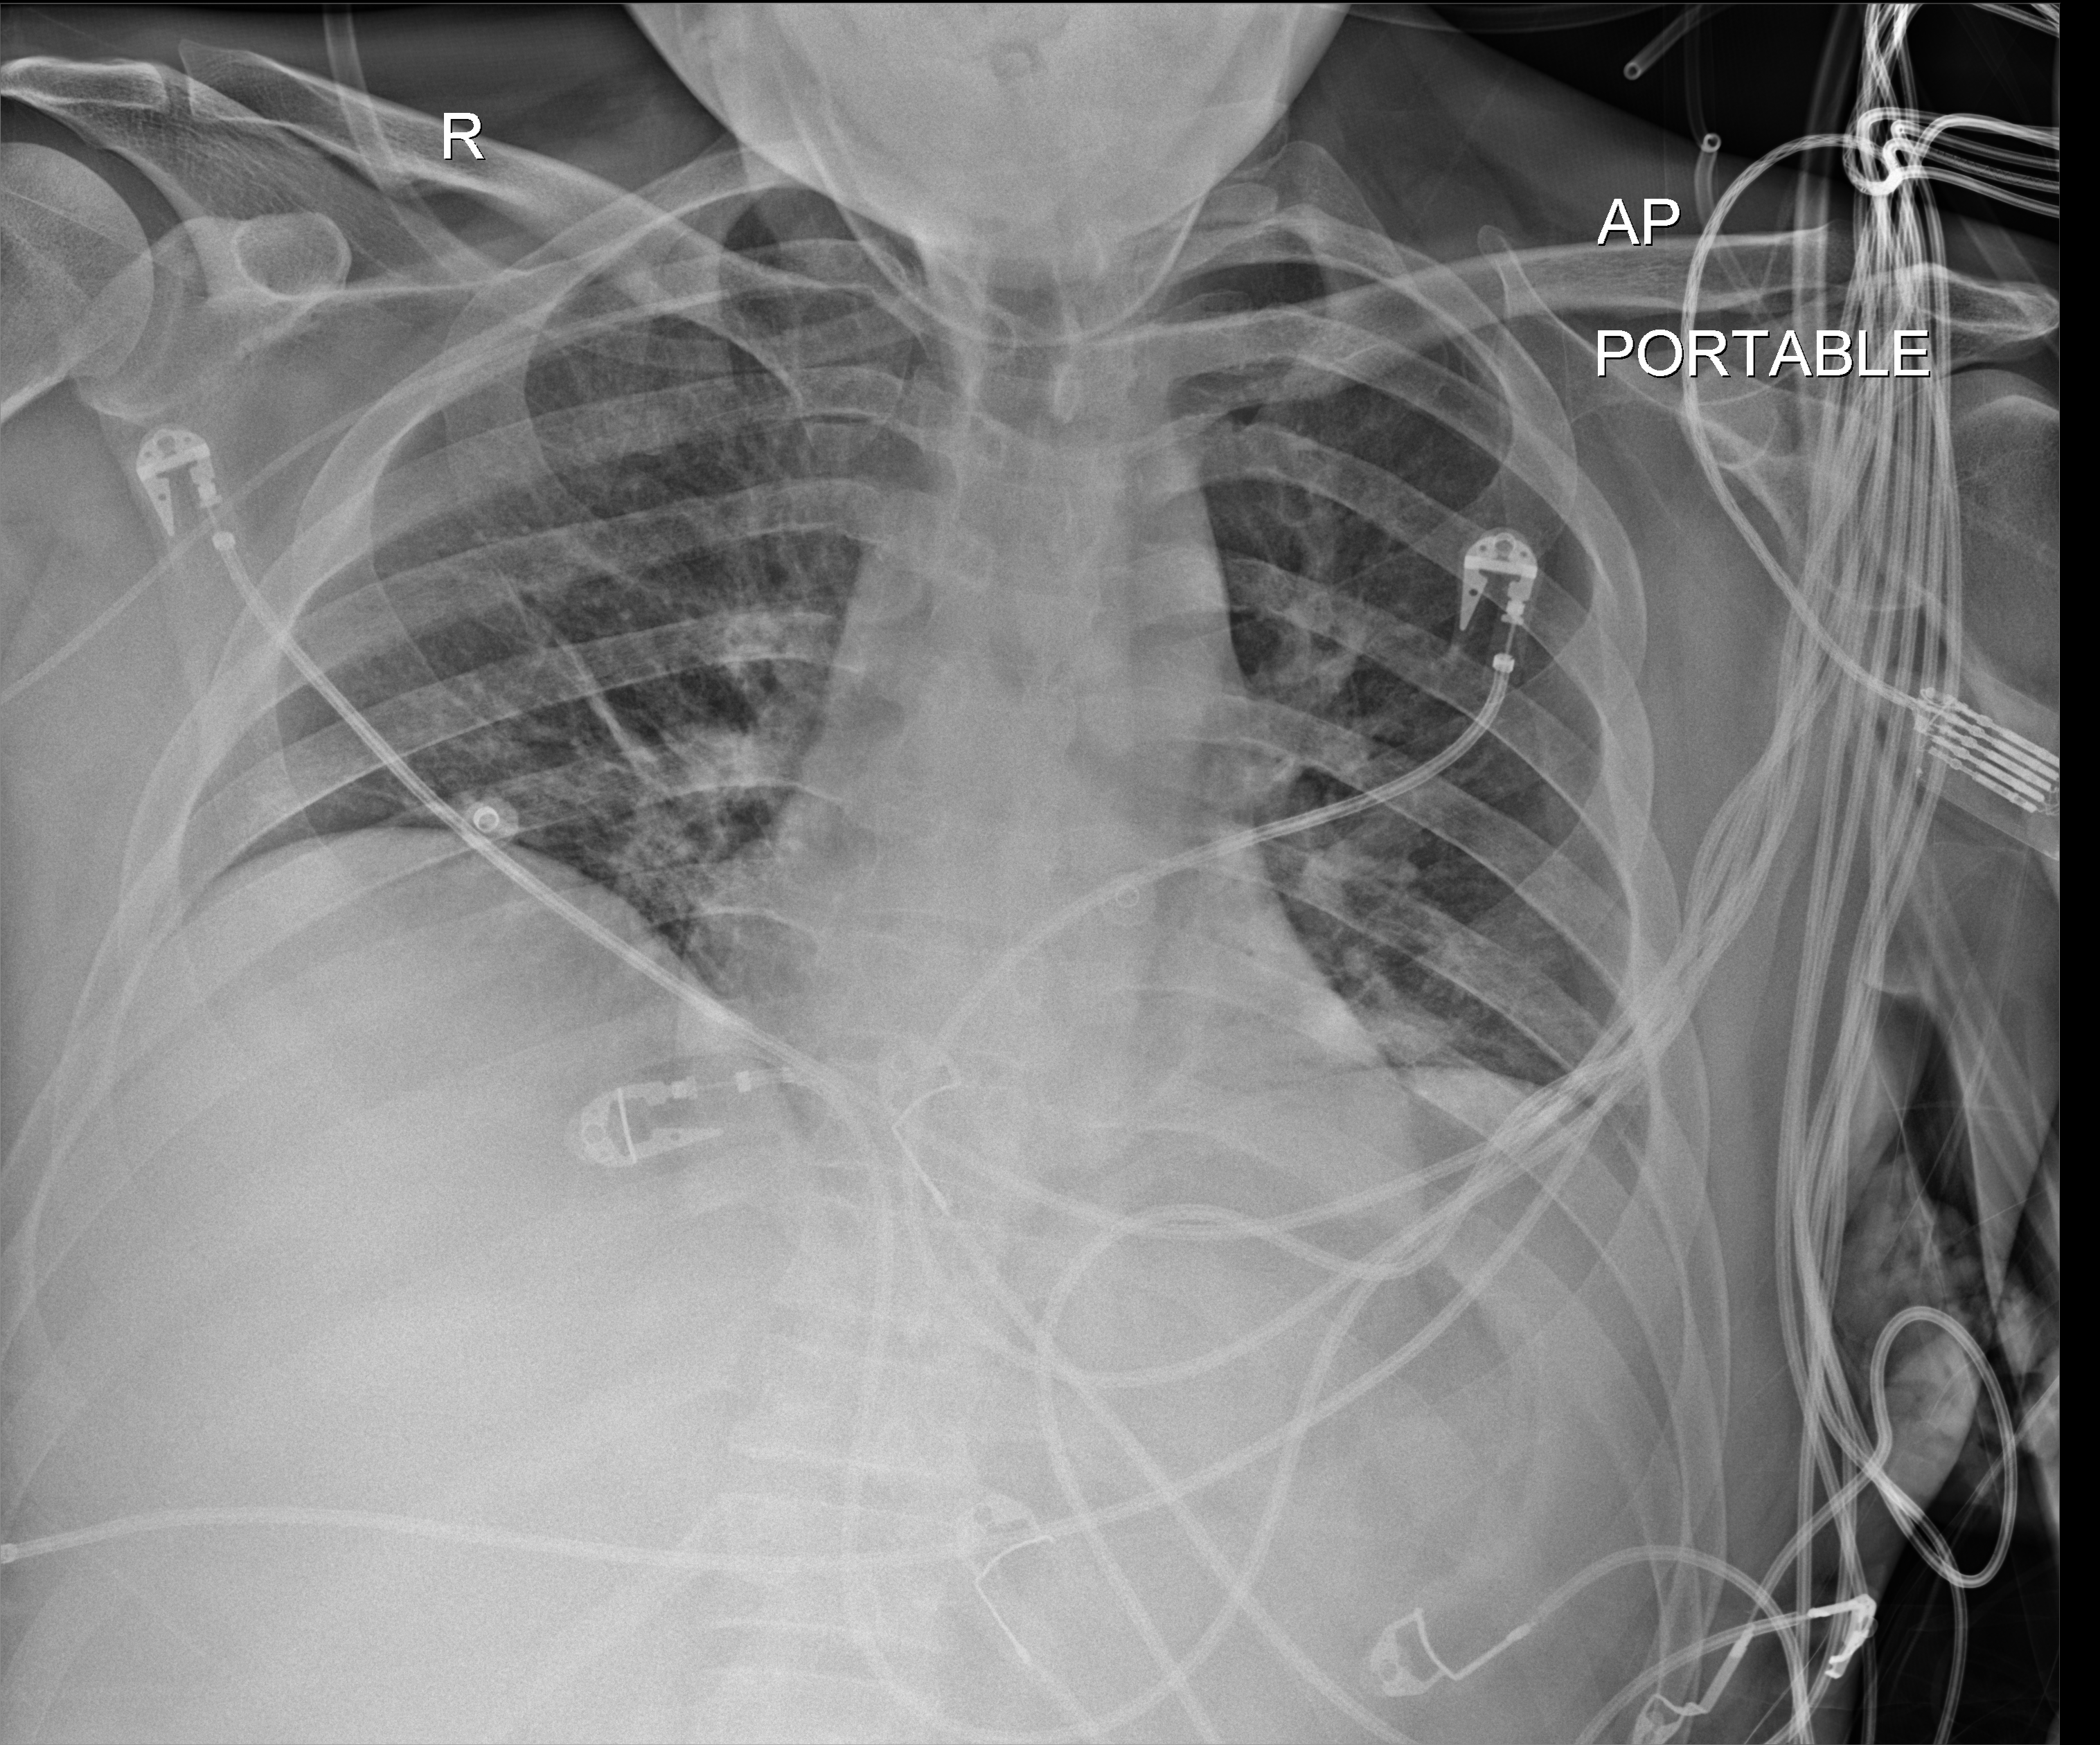
Bedside chest radiograph (digital radiography). Male patient hospitalised with COVID-19, age 18–59 years.
From the hospital-stay record, not from the radiograph (when in the stay this image was taken is not recorded): admitted to intensive care during this hospital stay: yes; smoking status (admission record): current; mechanically ventilated during this hospital stay: yes.